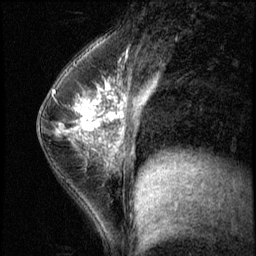
Breast MRI (dynamic contrast-enhanced), one sagittal slice. Position 33 of 56 along the scan axis. 3 images stored at this slice position (order not interpretable as contrast timing). 1.5 T. TE 4.2 ms, TR 8.7 ms. 2.5 mm slice thickness. 256 × 256 image matrix, field of view 180 × 180 mm. Female patient, age 35 years. Case-level facts recorded for this patient, not image findings: setting: breast cancer imaged before/during neoadjuvant chemotherapy; receptor status: HER2-positive.
Annotated regions visible in this slice (semi-automatically segmented with operator editing):
- analysis volume of interest (the breast-tissue region the enhancement analysis was run in; not a lesion): bounding box <58,84,138,186> (left, top, right, bottom; pixels)
- tumour enhancement mask (voxels above the 140 % enhancement threshold inside the analysis volume of interest): <58,84,138,139>